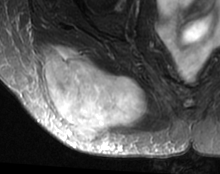
MRI of an extremity soft-tissue mass, one axial slice. Position 21 of 63 along the scan axis. T2-weighted fat-saturated. MR volume resampled by the dataset authors to the PET/CT grid (not the native acquisition matrix). 3.27 mm slice thickness. 220 × 174 image matrix, field of view 215 × 170 mm. Female patient. Case-level facts recorded for this patient, not image findings: histological type: spindle cell suggestive of myxofibrosarcoma; grade: intermediate; site of the primary tumour: right buttock.
Outlined on this slice (expert contour drawn on MRI and transferred to this co-registered scan by the dataset authors):
- gross tumour volume (mass): box from (x=43, y=45) to (x=149, y=142) px